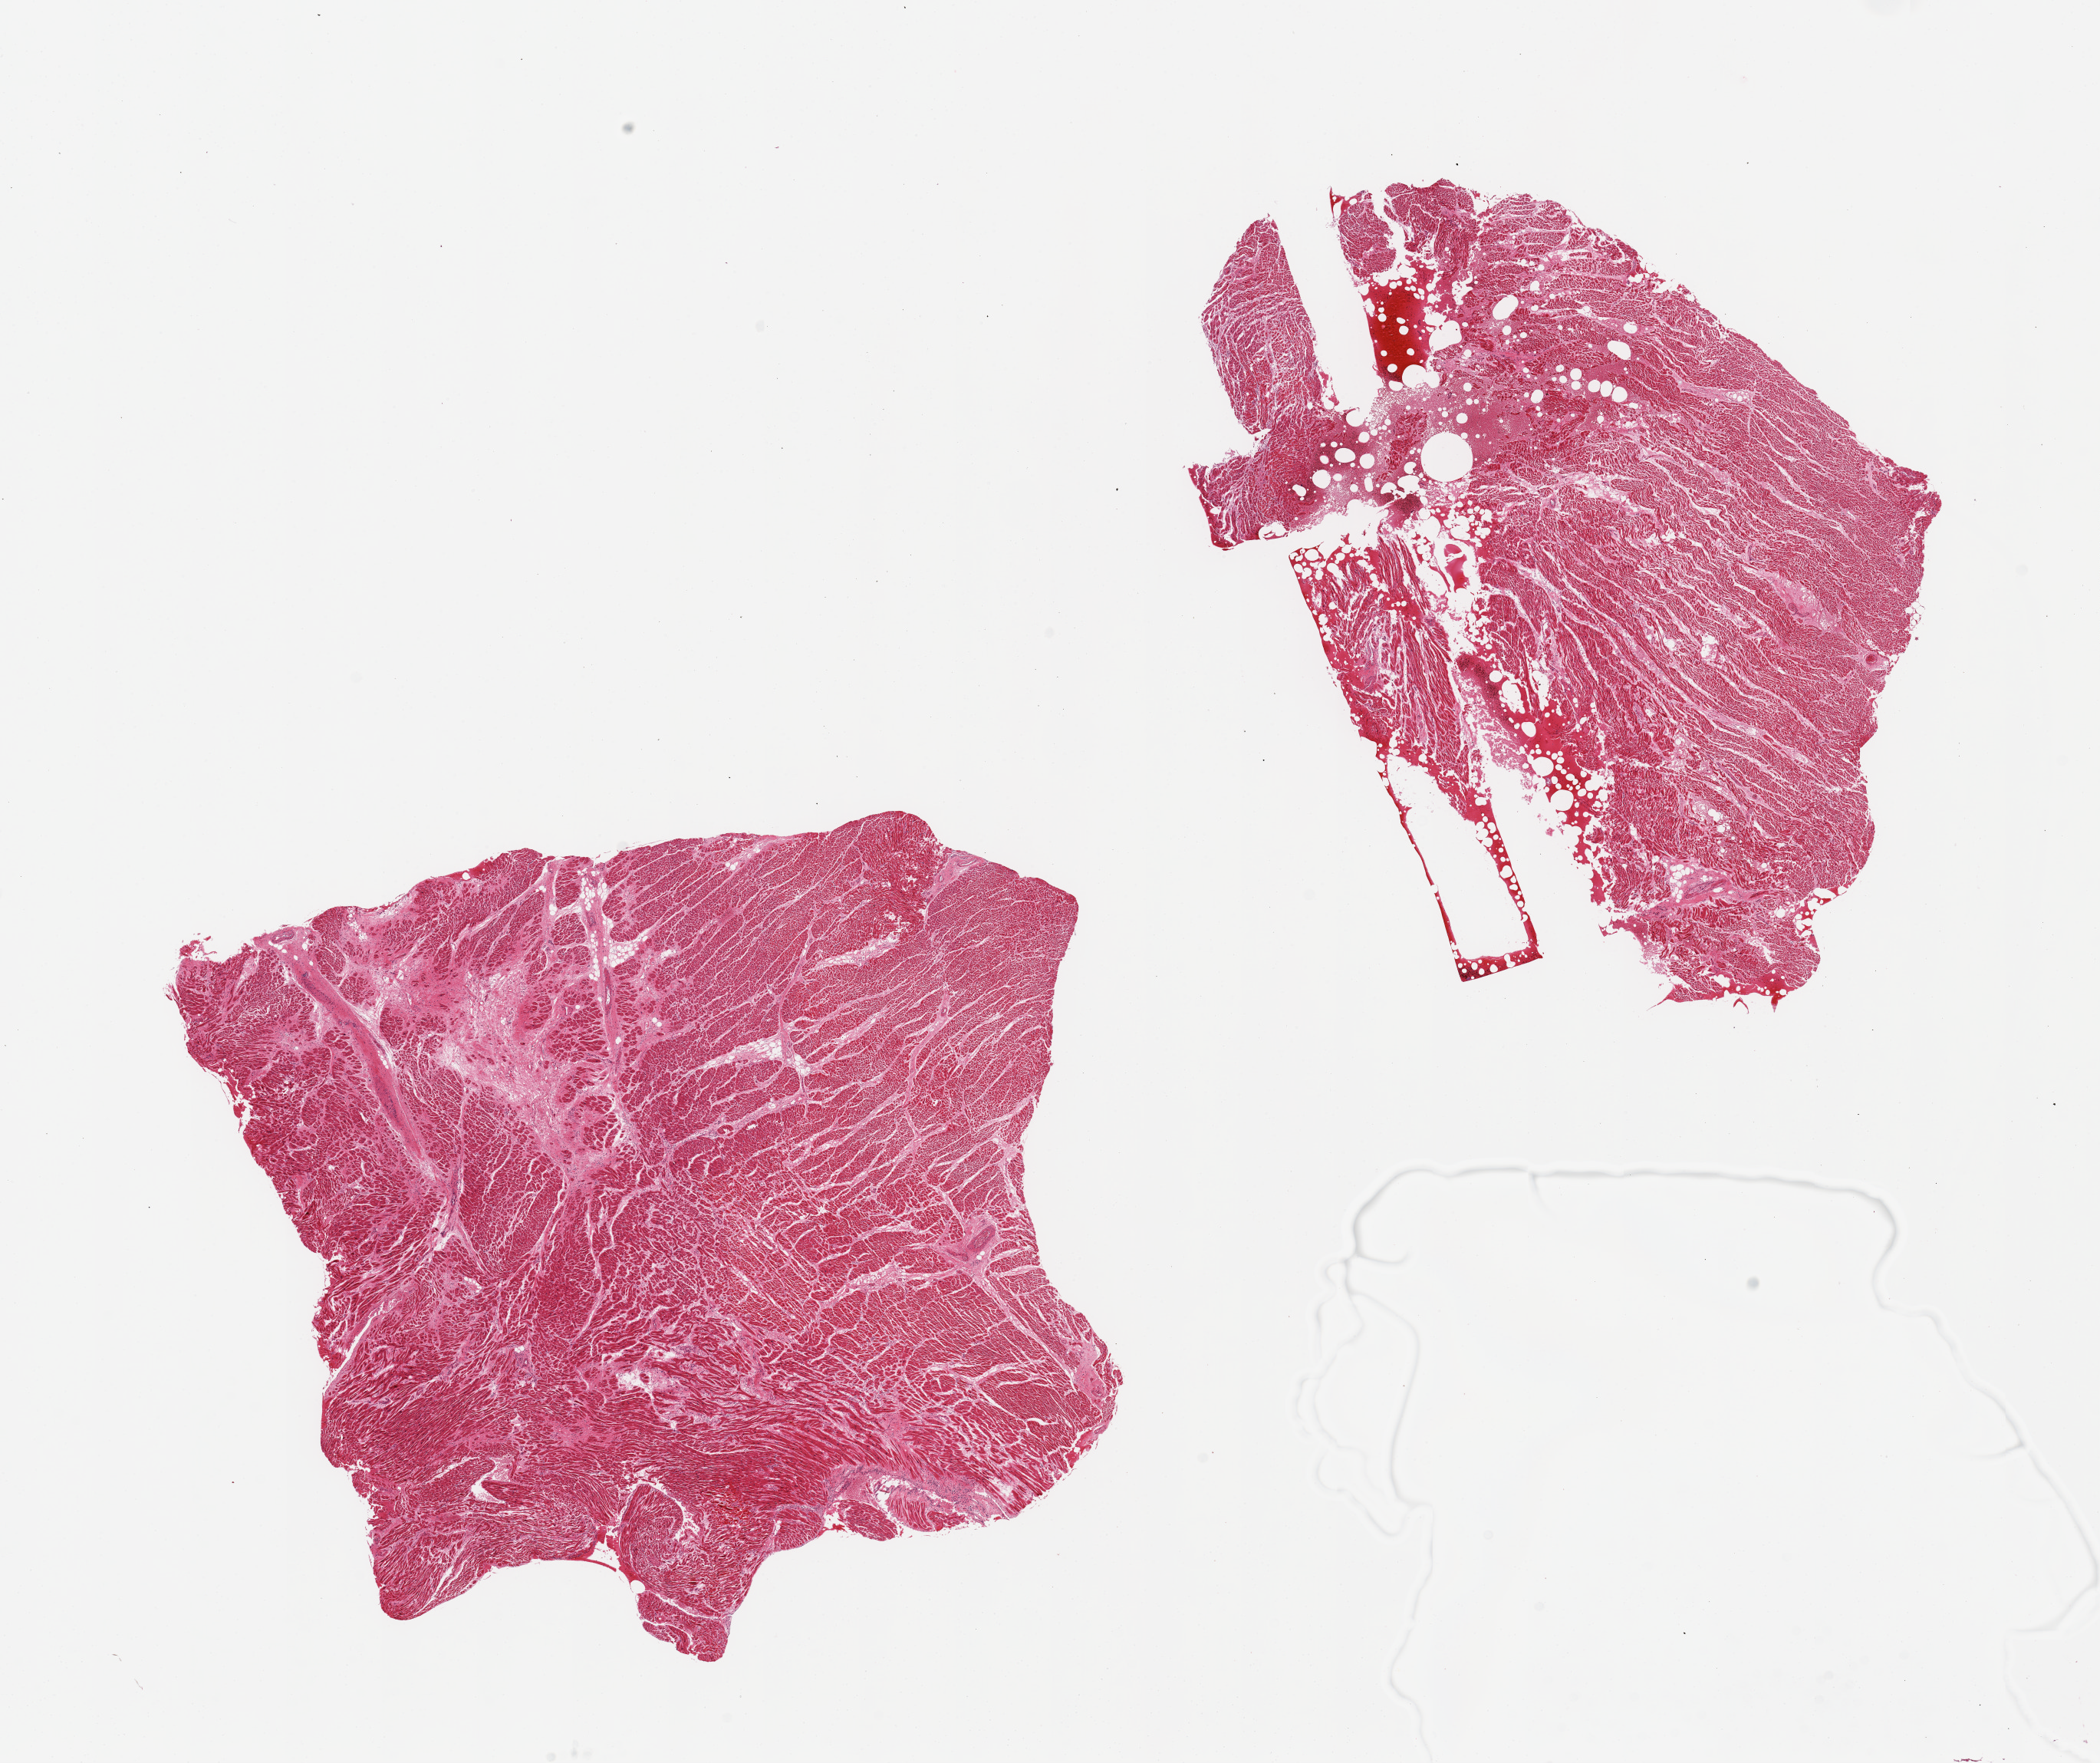
Digitized haematoxylin and eosin-stained section, low-resolution overview of the scanned area, about 21.7 x 18.2 mm (from a 20x scan), PAXgene-fixed paraffin-embedded (PFPE) section, sampled site (target tissue): heart, donor tissue sample. Female donor.
- reviewer comment on this tissue sample: 2 pieces; 1 with patchy scars consistent with old infarcts; other with areas of recent hemorrhage, 20%